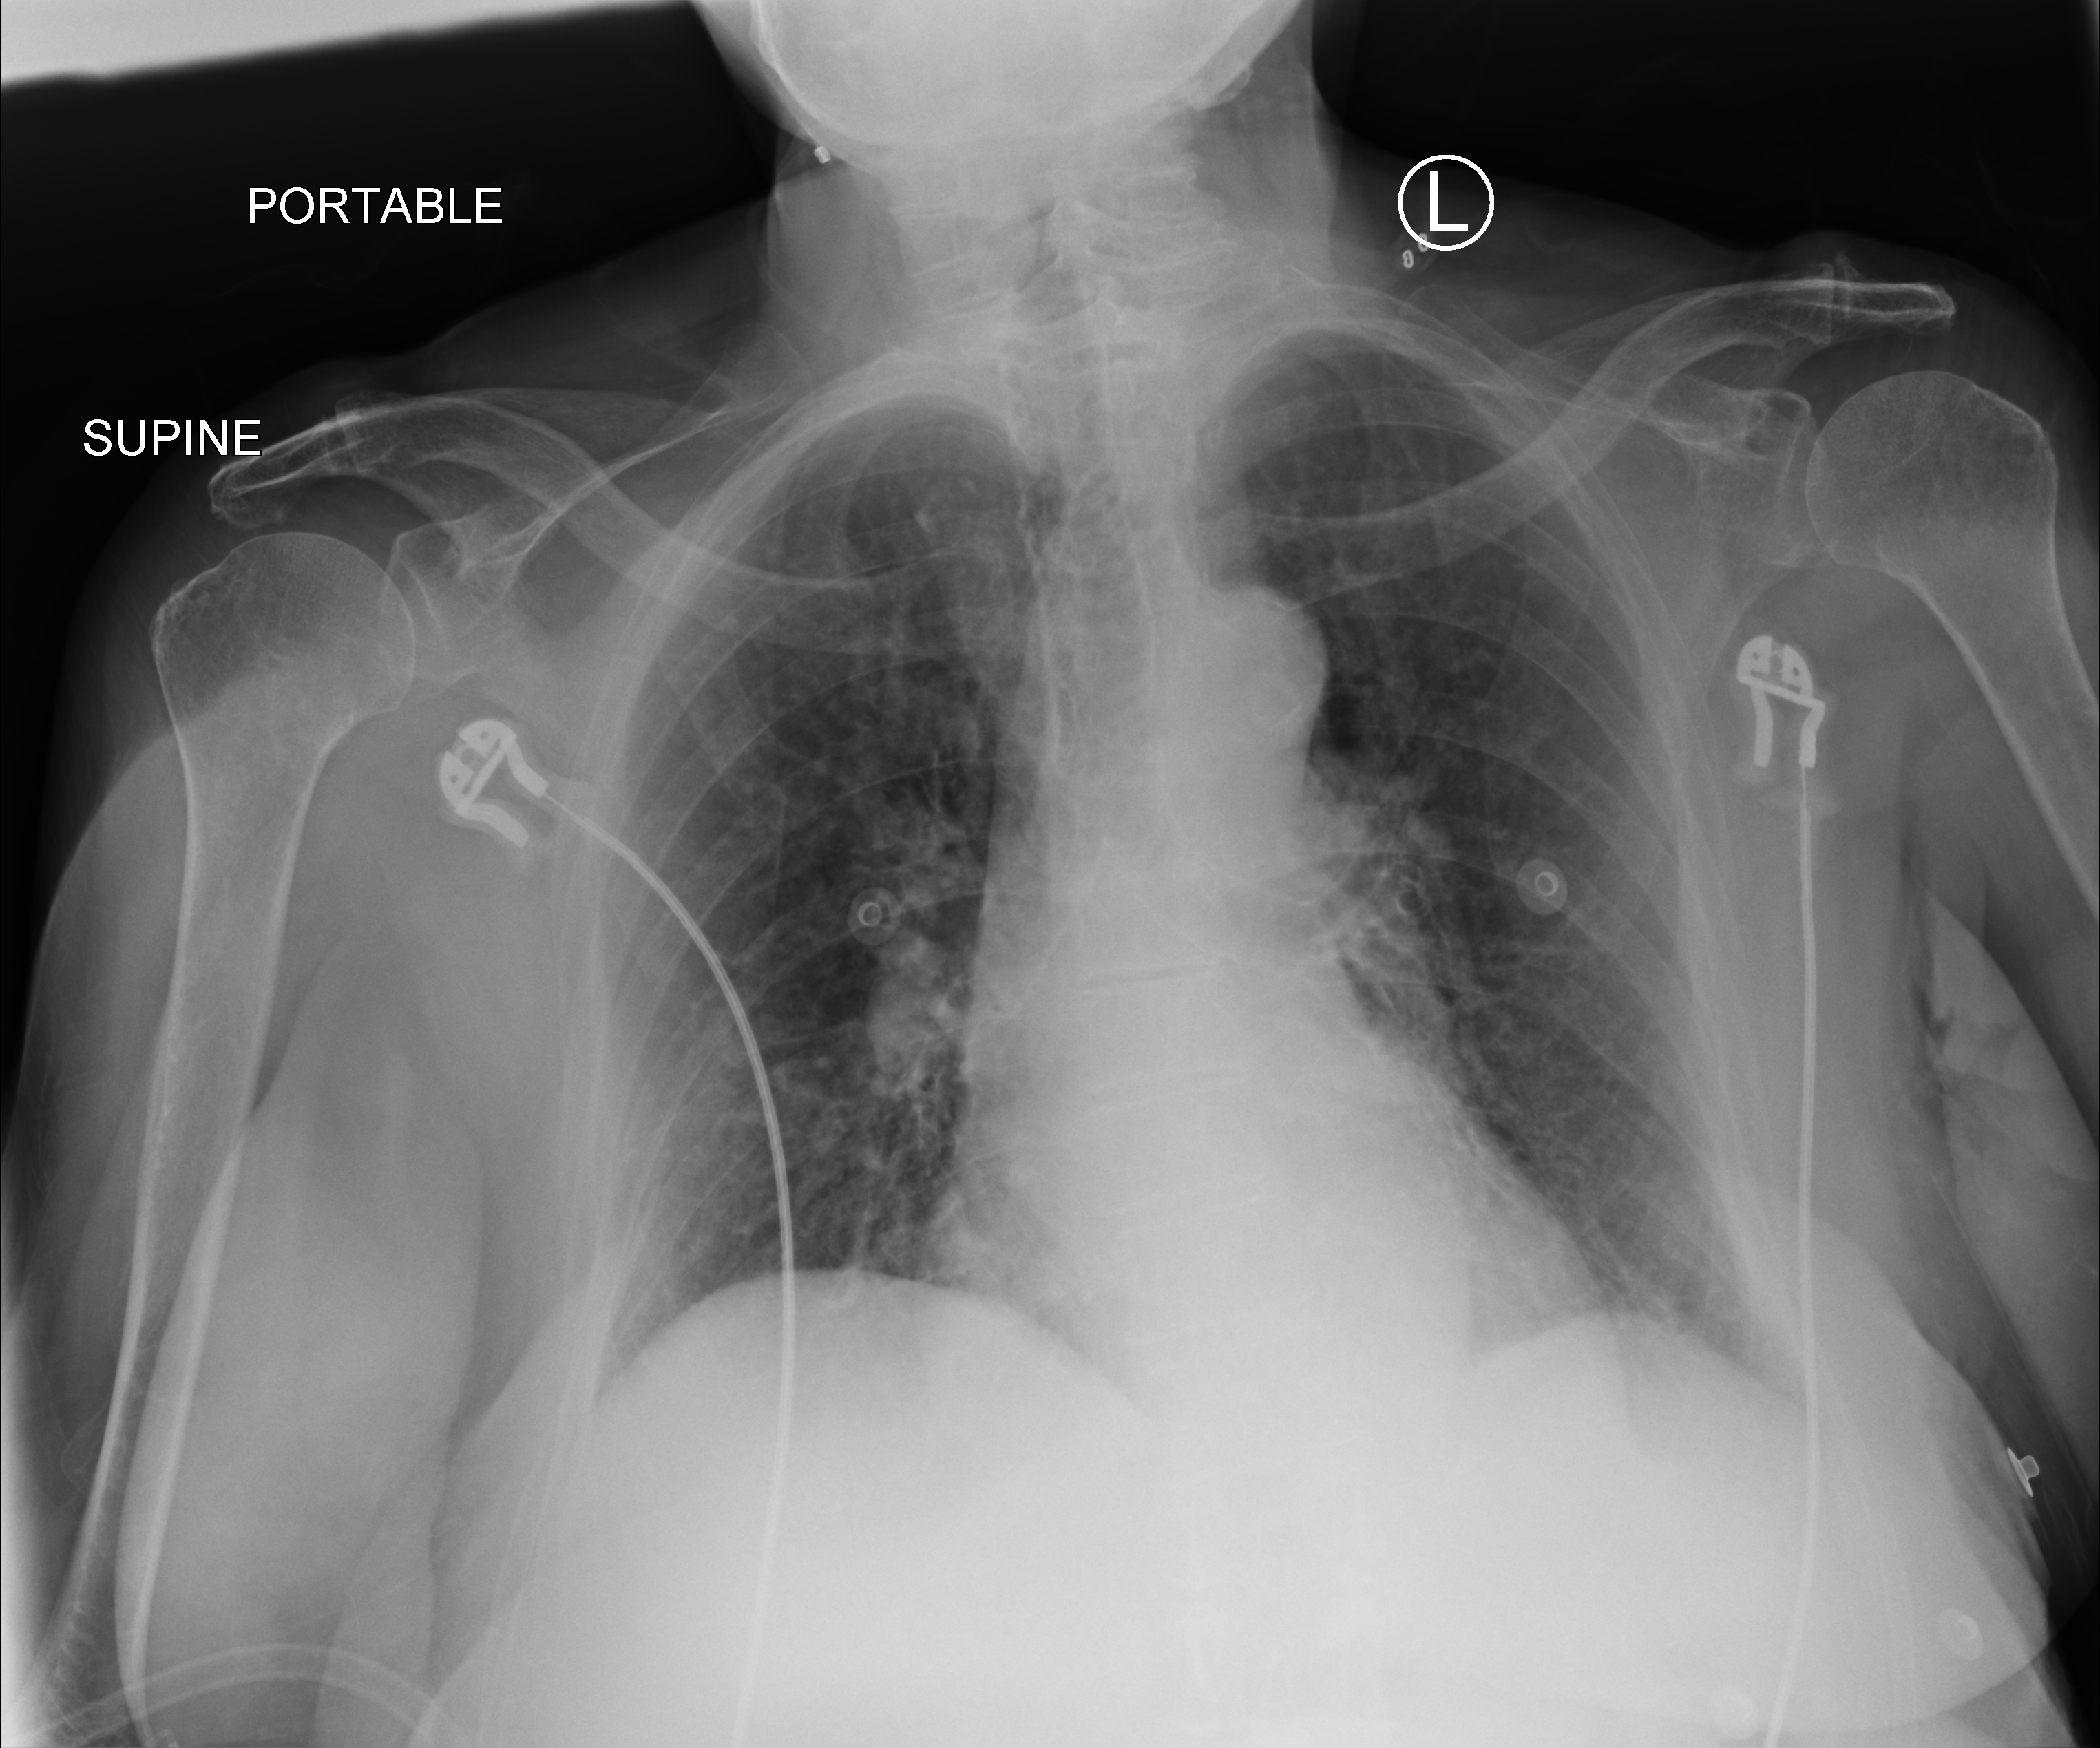
Bedside chest radiograph (computed radiography); anteroposterior (AP) projection. Patient hospitalised with COVID-19; female, aged 75–90 years.
Admission-level facts for this patient (not findings on this image; timing relative to this image not recorded):
- admitted to intensive care during this hospital stay: no
- smoking status (admission record): never